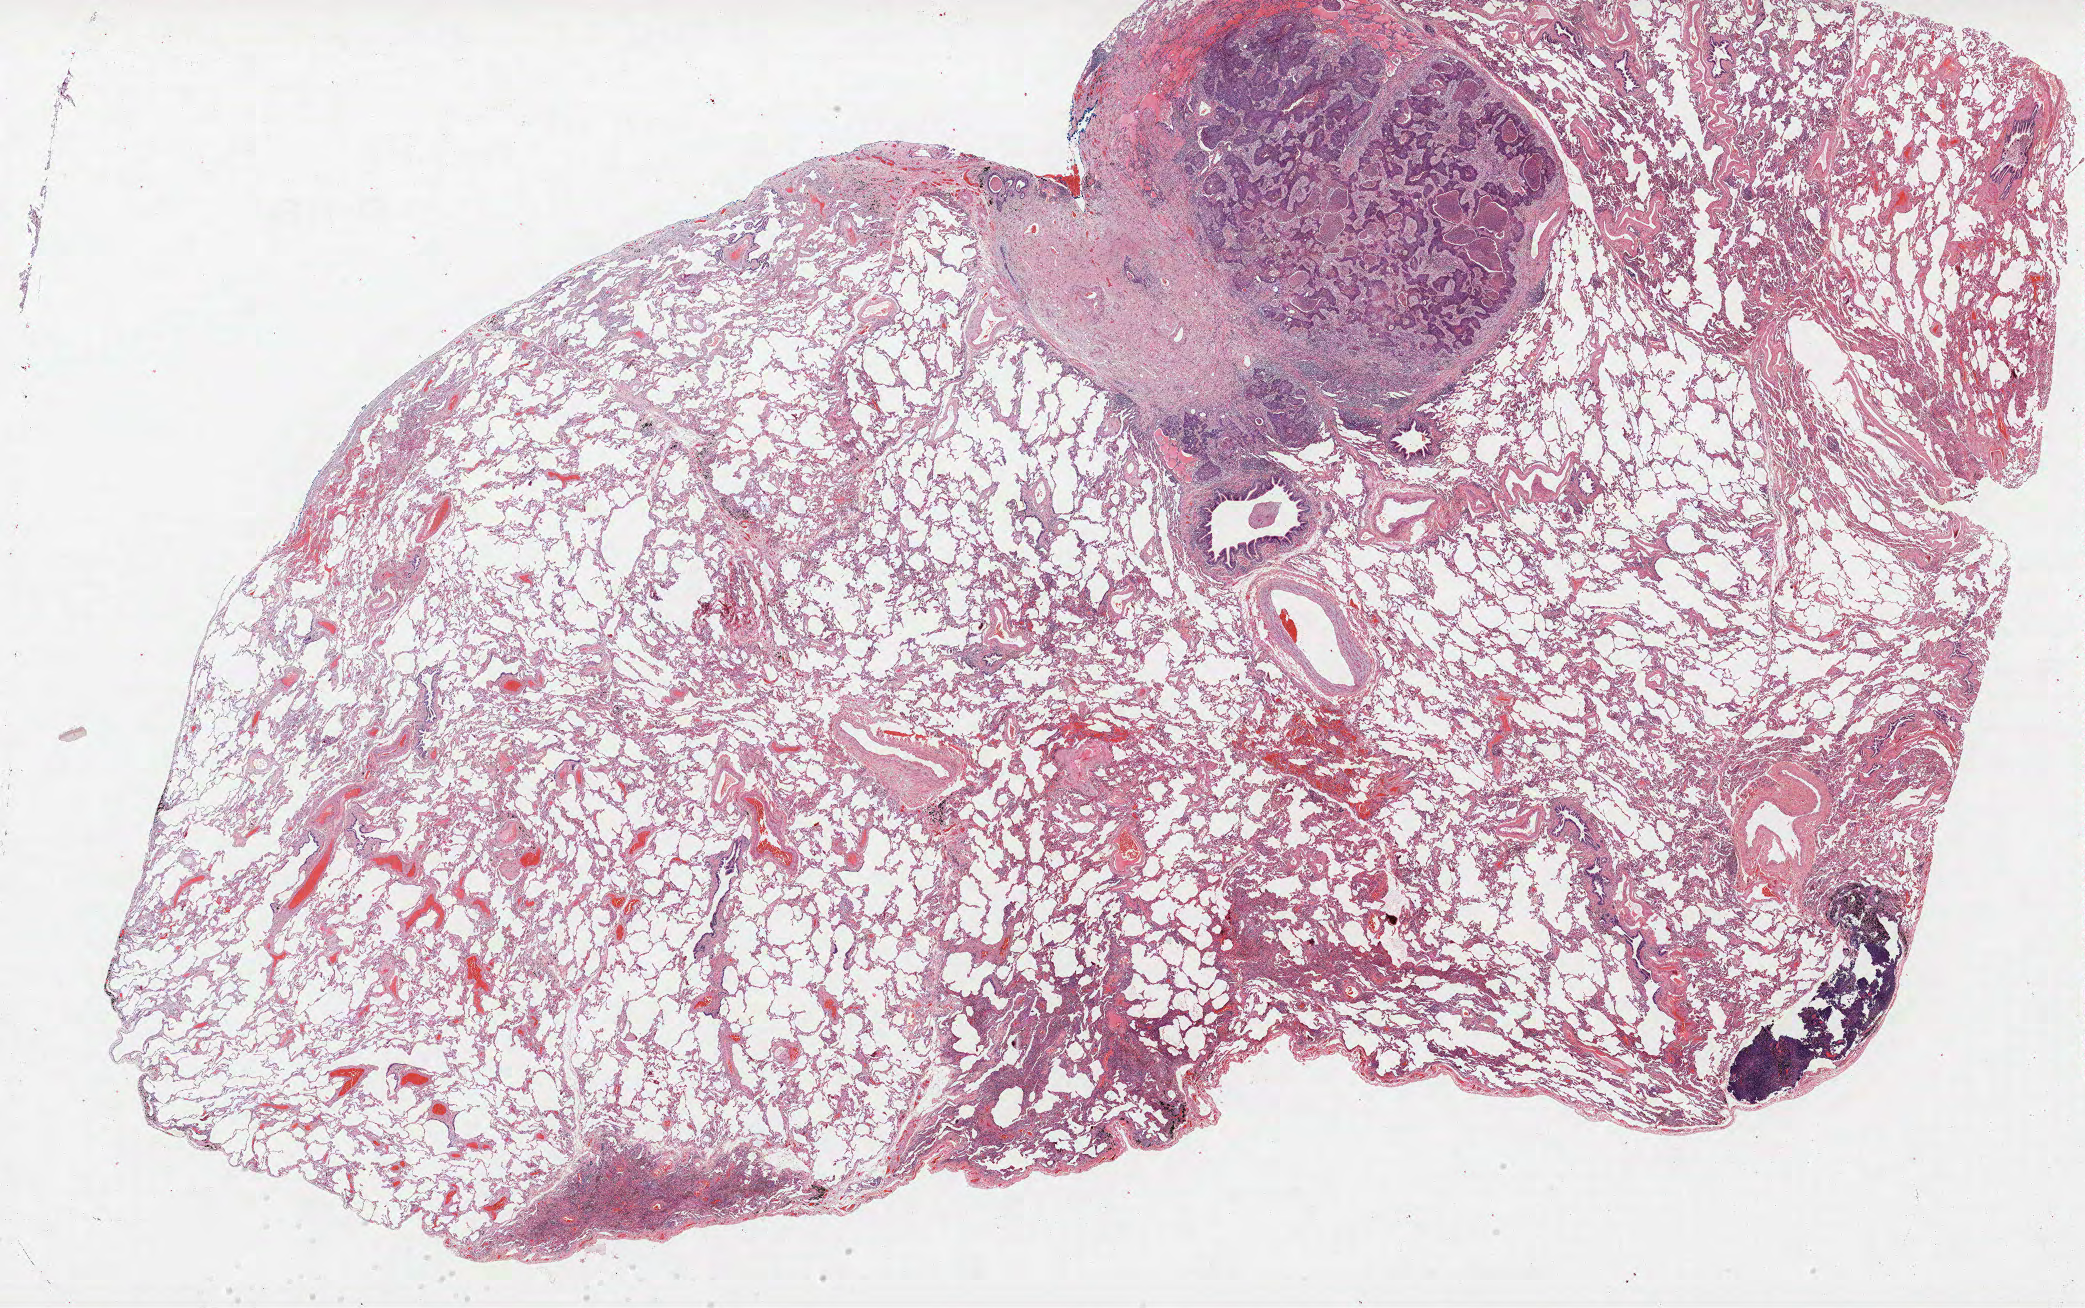
Whole-slide histology image, H&E-stained, low-resolution overview of the scanned area, about 33.4 x 20.9 mm (acquisition: 40x scan), formalin-fixed paraffin-embedded (FFPE) section, lung. Male, age 69 at enrolment. Current smoker at enrolment. Grade: poorly differentiated (G3).
Stage (AJCC 6th edition): IA. ICD-O-3 topography: upper lobe of lung (C34.1). Primary tumour location (clinical record): right upper lobe. Tumour size (pathology): 7 mm. Participant's lung-cancer diagnosis: Squamous cell carcinoma, large cell, nonkeratinizing, NOS (ICD-O-3 8072/3).